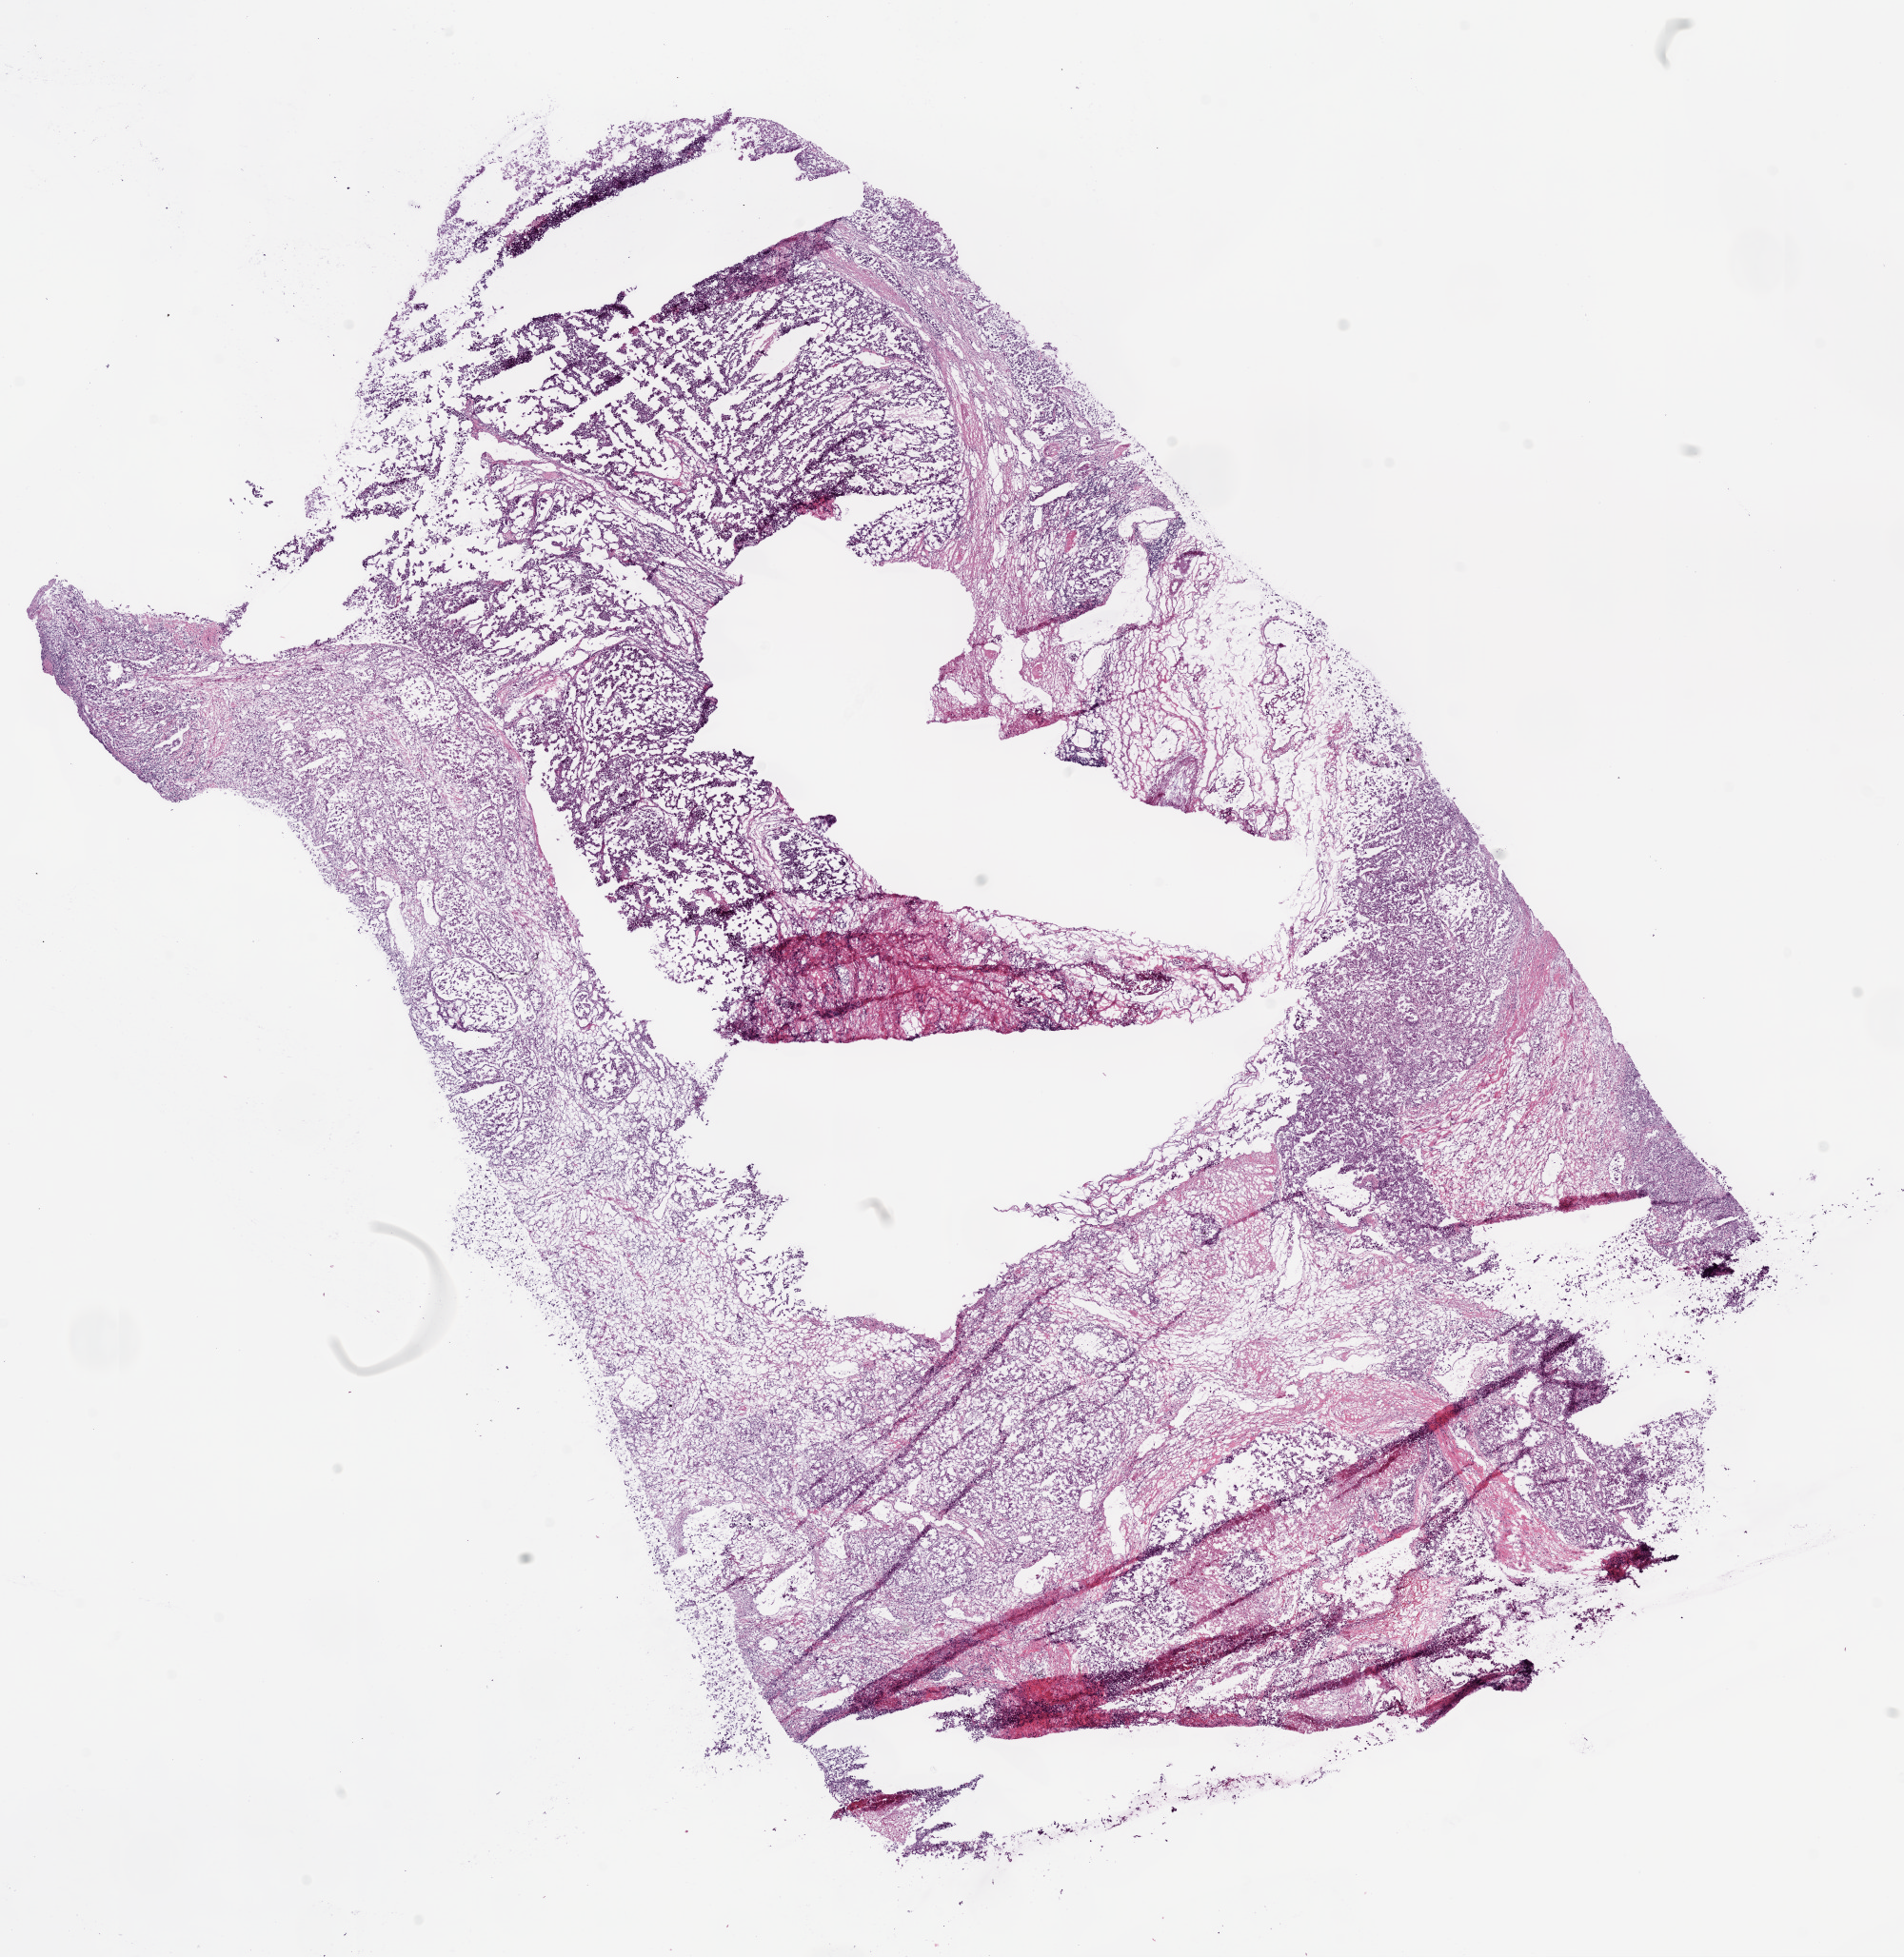
Digitized Hematoxylin and eosin (H&E) stained tissue section (whole slide) — whole scanned area (about 16.0 x 16.5 mm) shown as a low-resolution overview; frozen section from the bottom of the tissue portion; sample: primary tumour, kidney. Patient: female, age at initial diagnosis 76 years. Histologic grade: G4 (undifferentiated). Slide review estimates, as recorded: tumour cells 75%, tumour nuclei 70%, normal cells 0%, stromal cells 25%, necrosis 0%.
• laterality: left
• AJCC pathologic stage: III
• lymph nodes positive (case pathology): 0 of 4 examined
• histologic diagnosis: Clear cell adenocarcinoma, NOS